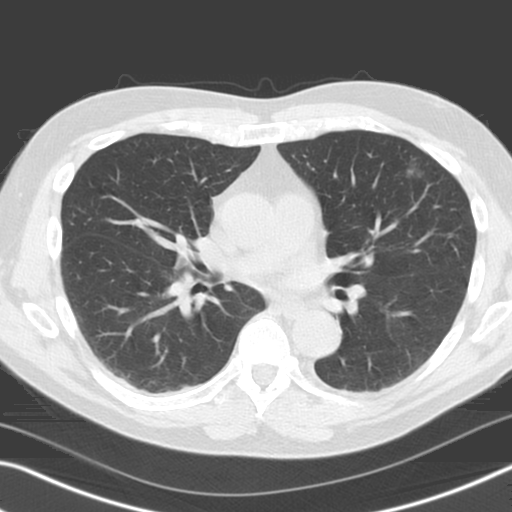
Axial slice from a low-dose chest CT screening exam, baseline screening round, lung window (W 1500 / L -600 HU). Male, age 71 years at enrolment. Former smoker at enrolment.
Expert-annotated lung lesion, bounding box [x1, y1, x2, y2] px = [397, 149, 435, 187]. Screening reader's record for this exam (one nodule recorded; not confirmed to be the boxed lesion): non-calcified nodule or mass ≥4 mm, left upper lobe, 11 × 10 mm, poorly defined margins, ground glass attenuation. Lung cancer was diagnosed 289 days after this screen: adenocarcinoma, NOS, left upper lobe, moderately differentiated (G2), stage IA (AJCC 6th edition), 11 mm at pathology.